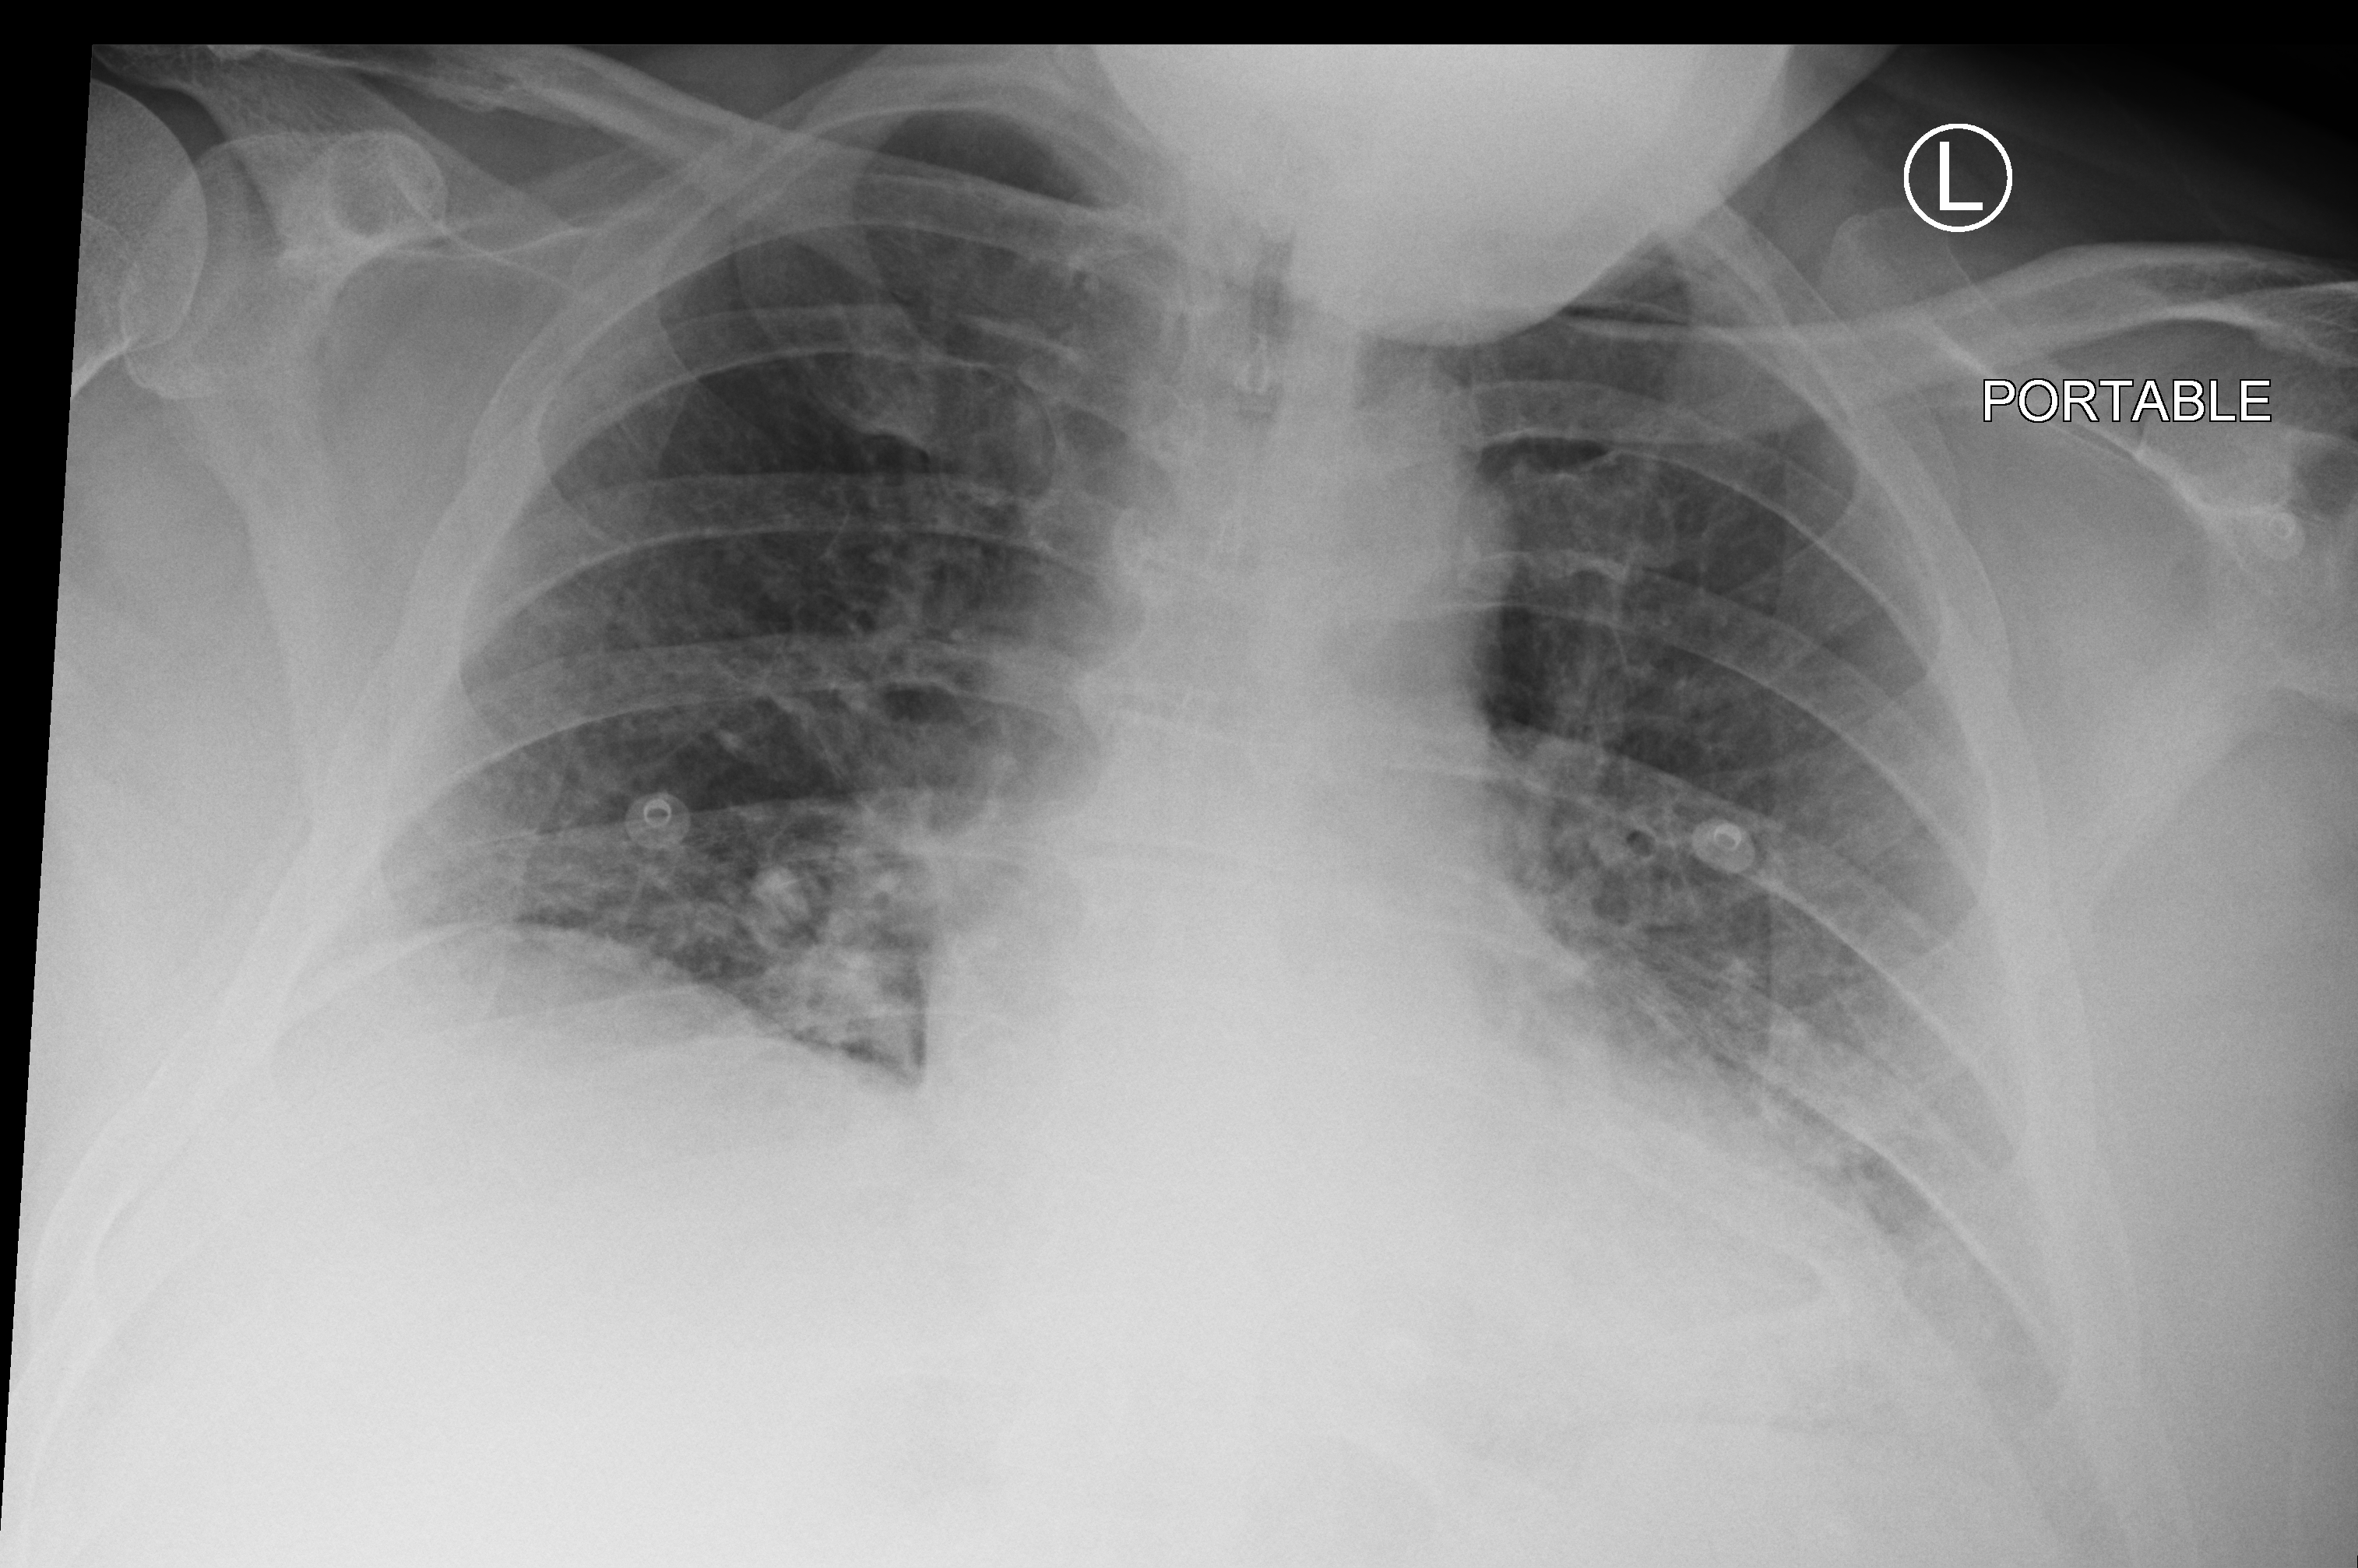
Chest X-ray (portable). Male patient hospitalised with COVID-19, age 60–74 years.
Admission-level facts for this patient (not findings on this image; timing relative to this image not recorded):
- other chronic lung disease (admission record): no
- diabetes (admission record): no